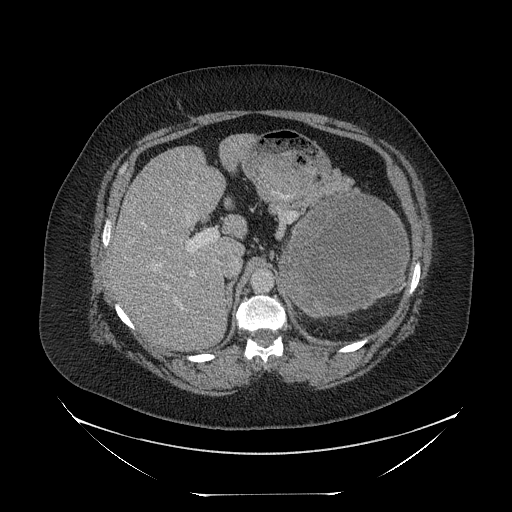
Contrast-enhanced abdominal CT, one axial slice; slice 154 of 205 in the series (ordered by position); reconstruction kernel STANDARD; 120 kVp; intravenous contrast given; soft-tissue window (W 400 / L 40 HU); 2.5 mm slice thickness; 512 × 512 image matrix. Female patient, age 53 years. From the clinical record (not read from this slice): diagnosis: adrenocortical carcinoma; tumour side: left adrenal; tumour size at pathology: 17 cm; Ki-67 index: 20 %; stage (as recorded): 3.
Structures marked on this image (semi-automatic segmentation, software-assisted and operator-edited):
- mass: bounding box (x1, y1, x2, y2) in pixels: (286, 194, 407, 316)